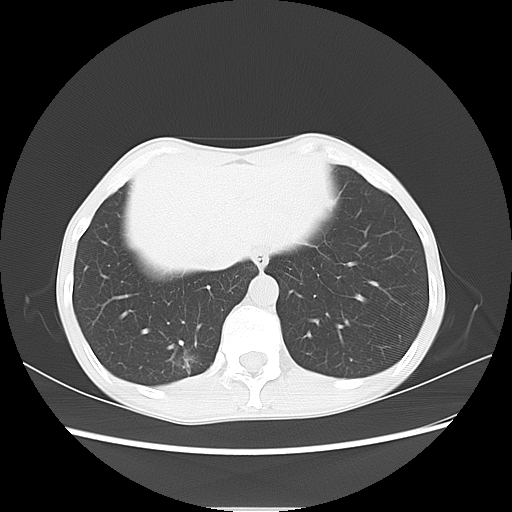
Chest CT, one axial slice. Position 16 of 69 along the scan axis. Reconstruction kernel LUNG. 120 kVp. Lung window (W 1500 / L -600 HU). 5 mm slice thickness. 512 × 512 image matrix, field of view 350 × 350 mm. Patient: female, 51 years. From the clinical record (not read from this slice): clinical TNM (as recorded): T1c N0 M0; histopathological grade: G2-3.
Outlined on this slice (bounding box drawn by a radiologist):
- lung tumour (recorded histology: adenocarcinoma): bounding box (x1, y1, x2, y2) in pixels: (167, 336, 199, 382)